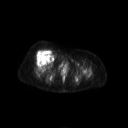
FDG PET of an extremity soft-tissue mass (from a PET/CT study), one axial slice; slice 60 of 267 in the series (ordered by position); 128 × 128 image matrix, field of view 700 × 700 mm. Patient: female, 56 years. Case-level facts recorded for this patient, not image findings: histological type: malignant solitary fibrous tumor; grade: intermediate; site of the primary tumour: right thigh.
Outlined on this slice (expert contour drawn on MRI and transferred to this co-registered scan by the dataset authors):
- gross tumour volume including surrounding oedema: bounding box [x1, y1, x2, y2] px = [35, 50, 51, 62]
- gross tumour volume (mass): [36, 50, 51, 62]